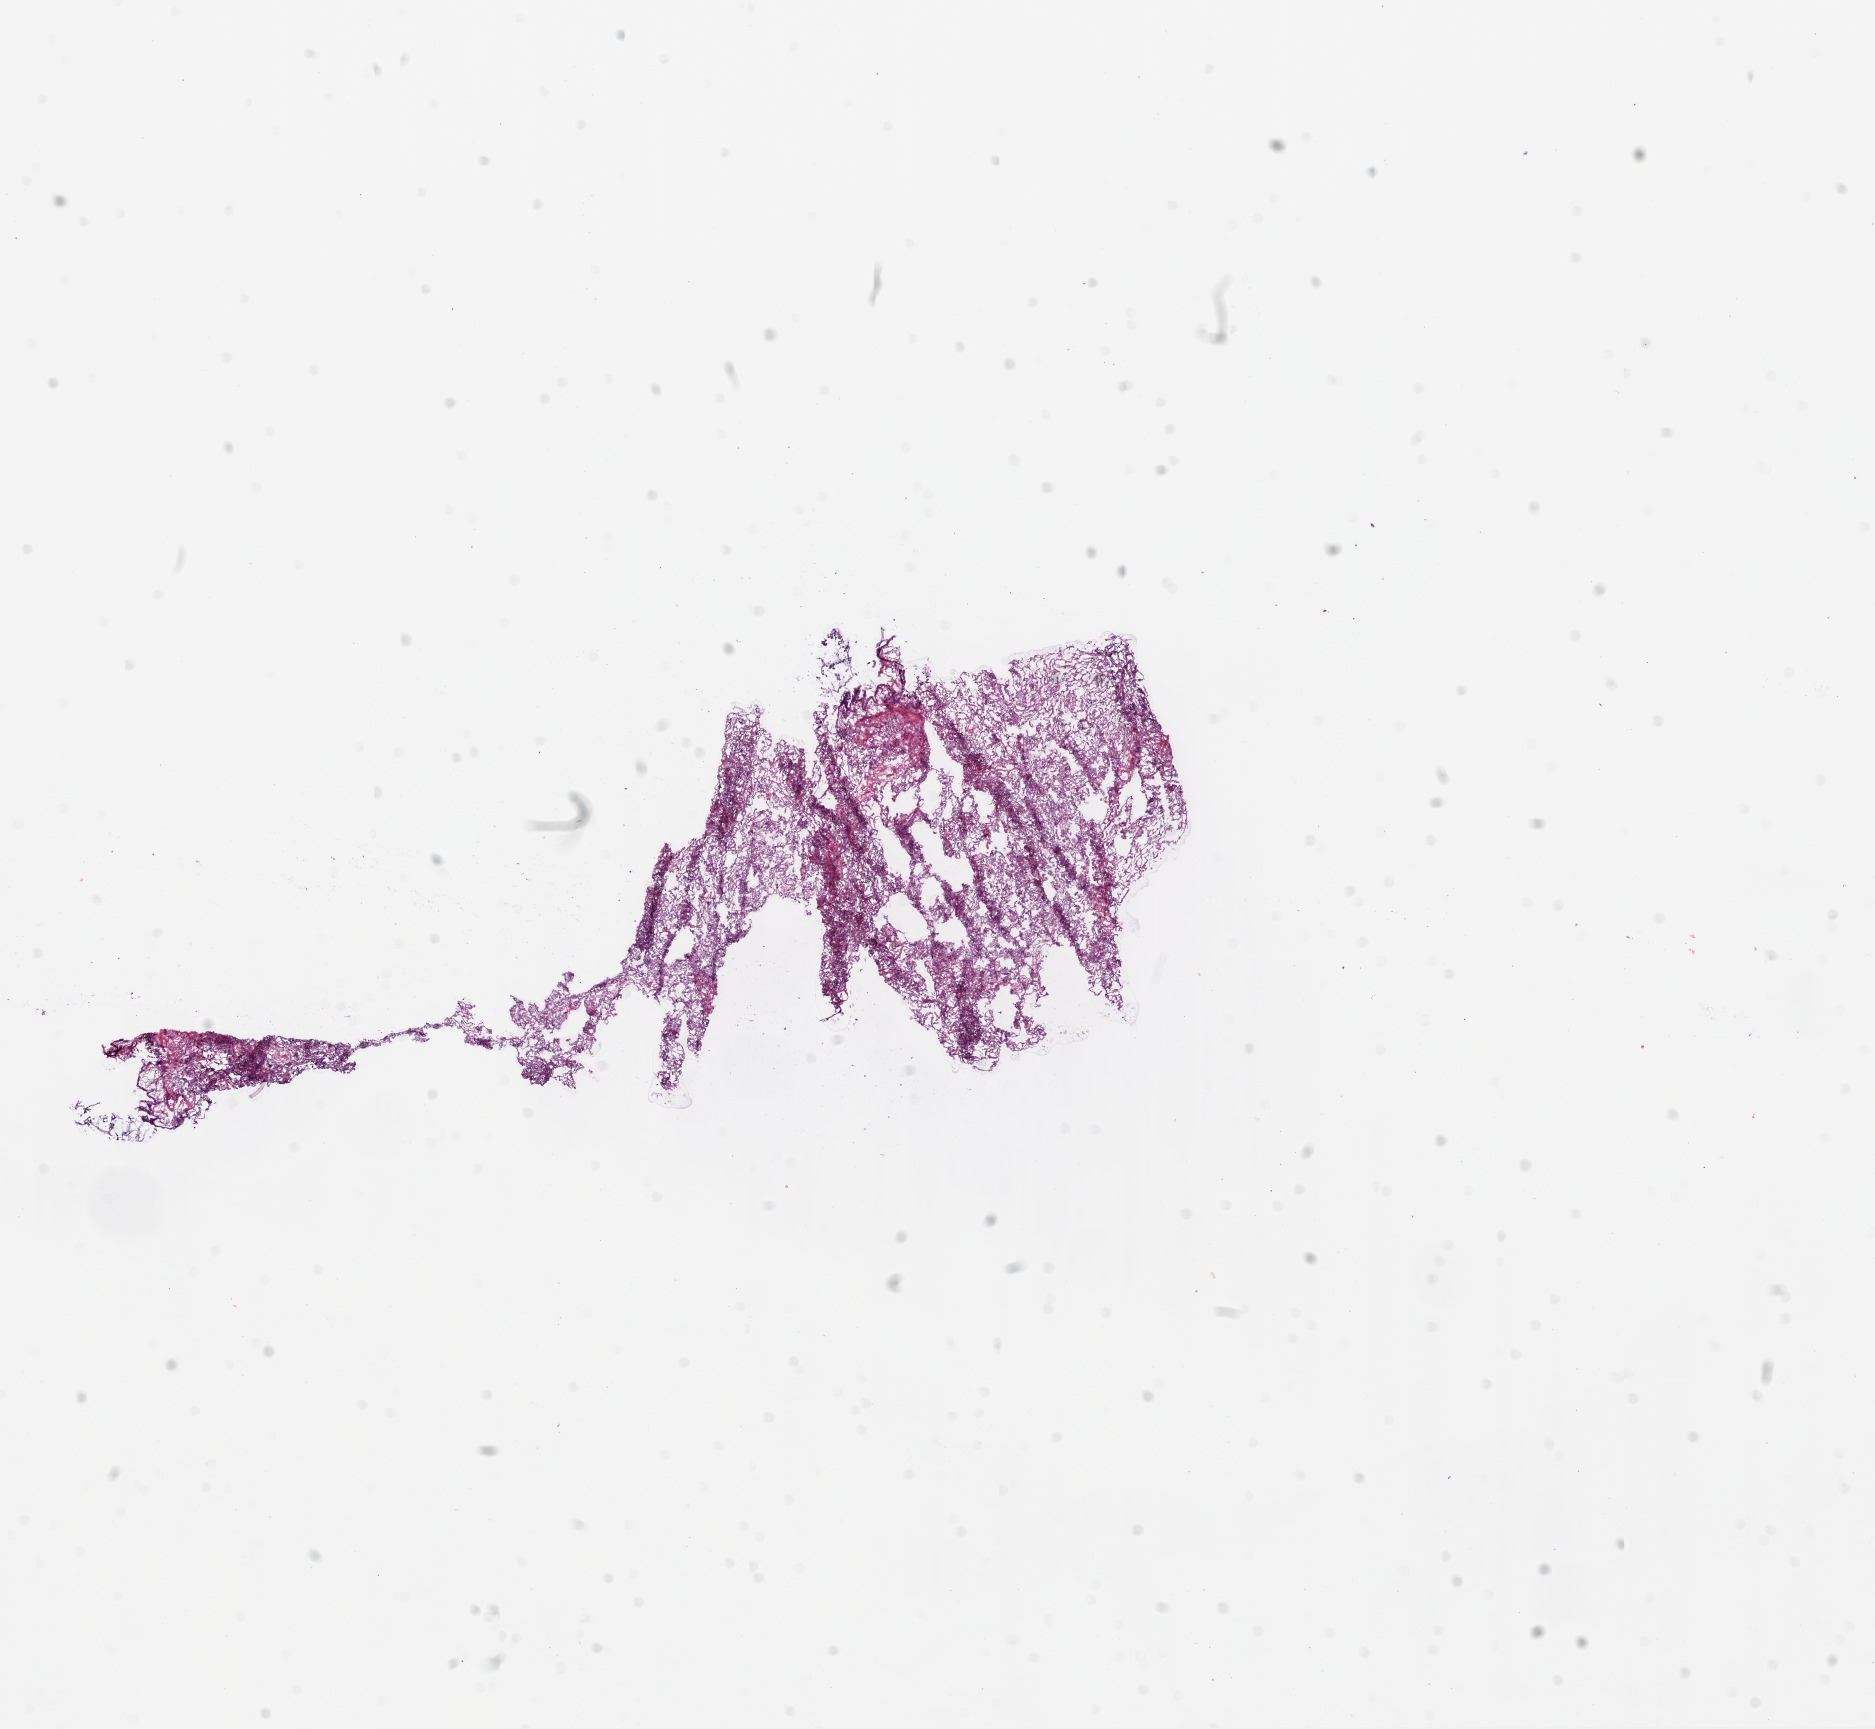
H&E whole-slide image — low-resolution overview of the scanned area, about 15.0 x 13.9 mm, frozen section from the top of the tissue portion, lung, solid tissue normal (non-tumour tissue) sample. Patient: male, age at initial diagnosis 65 years.
• this section: solid tissue normal (non-tumour) sample from the same patient
• patient diagnosis: Squamous cell carcinoma, NOS (lower lobe, lung)